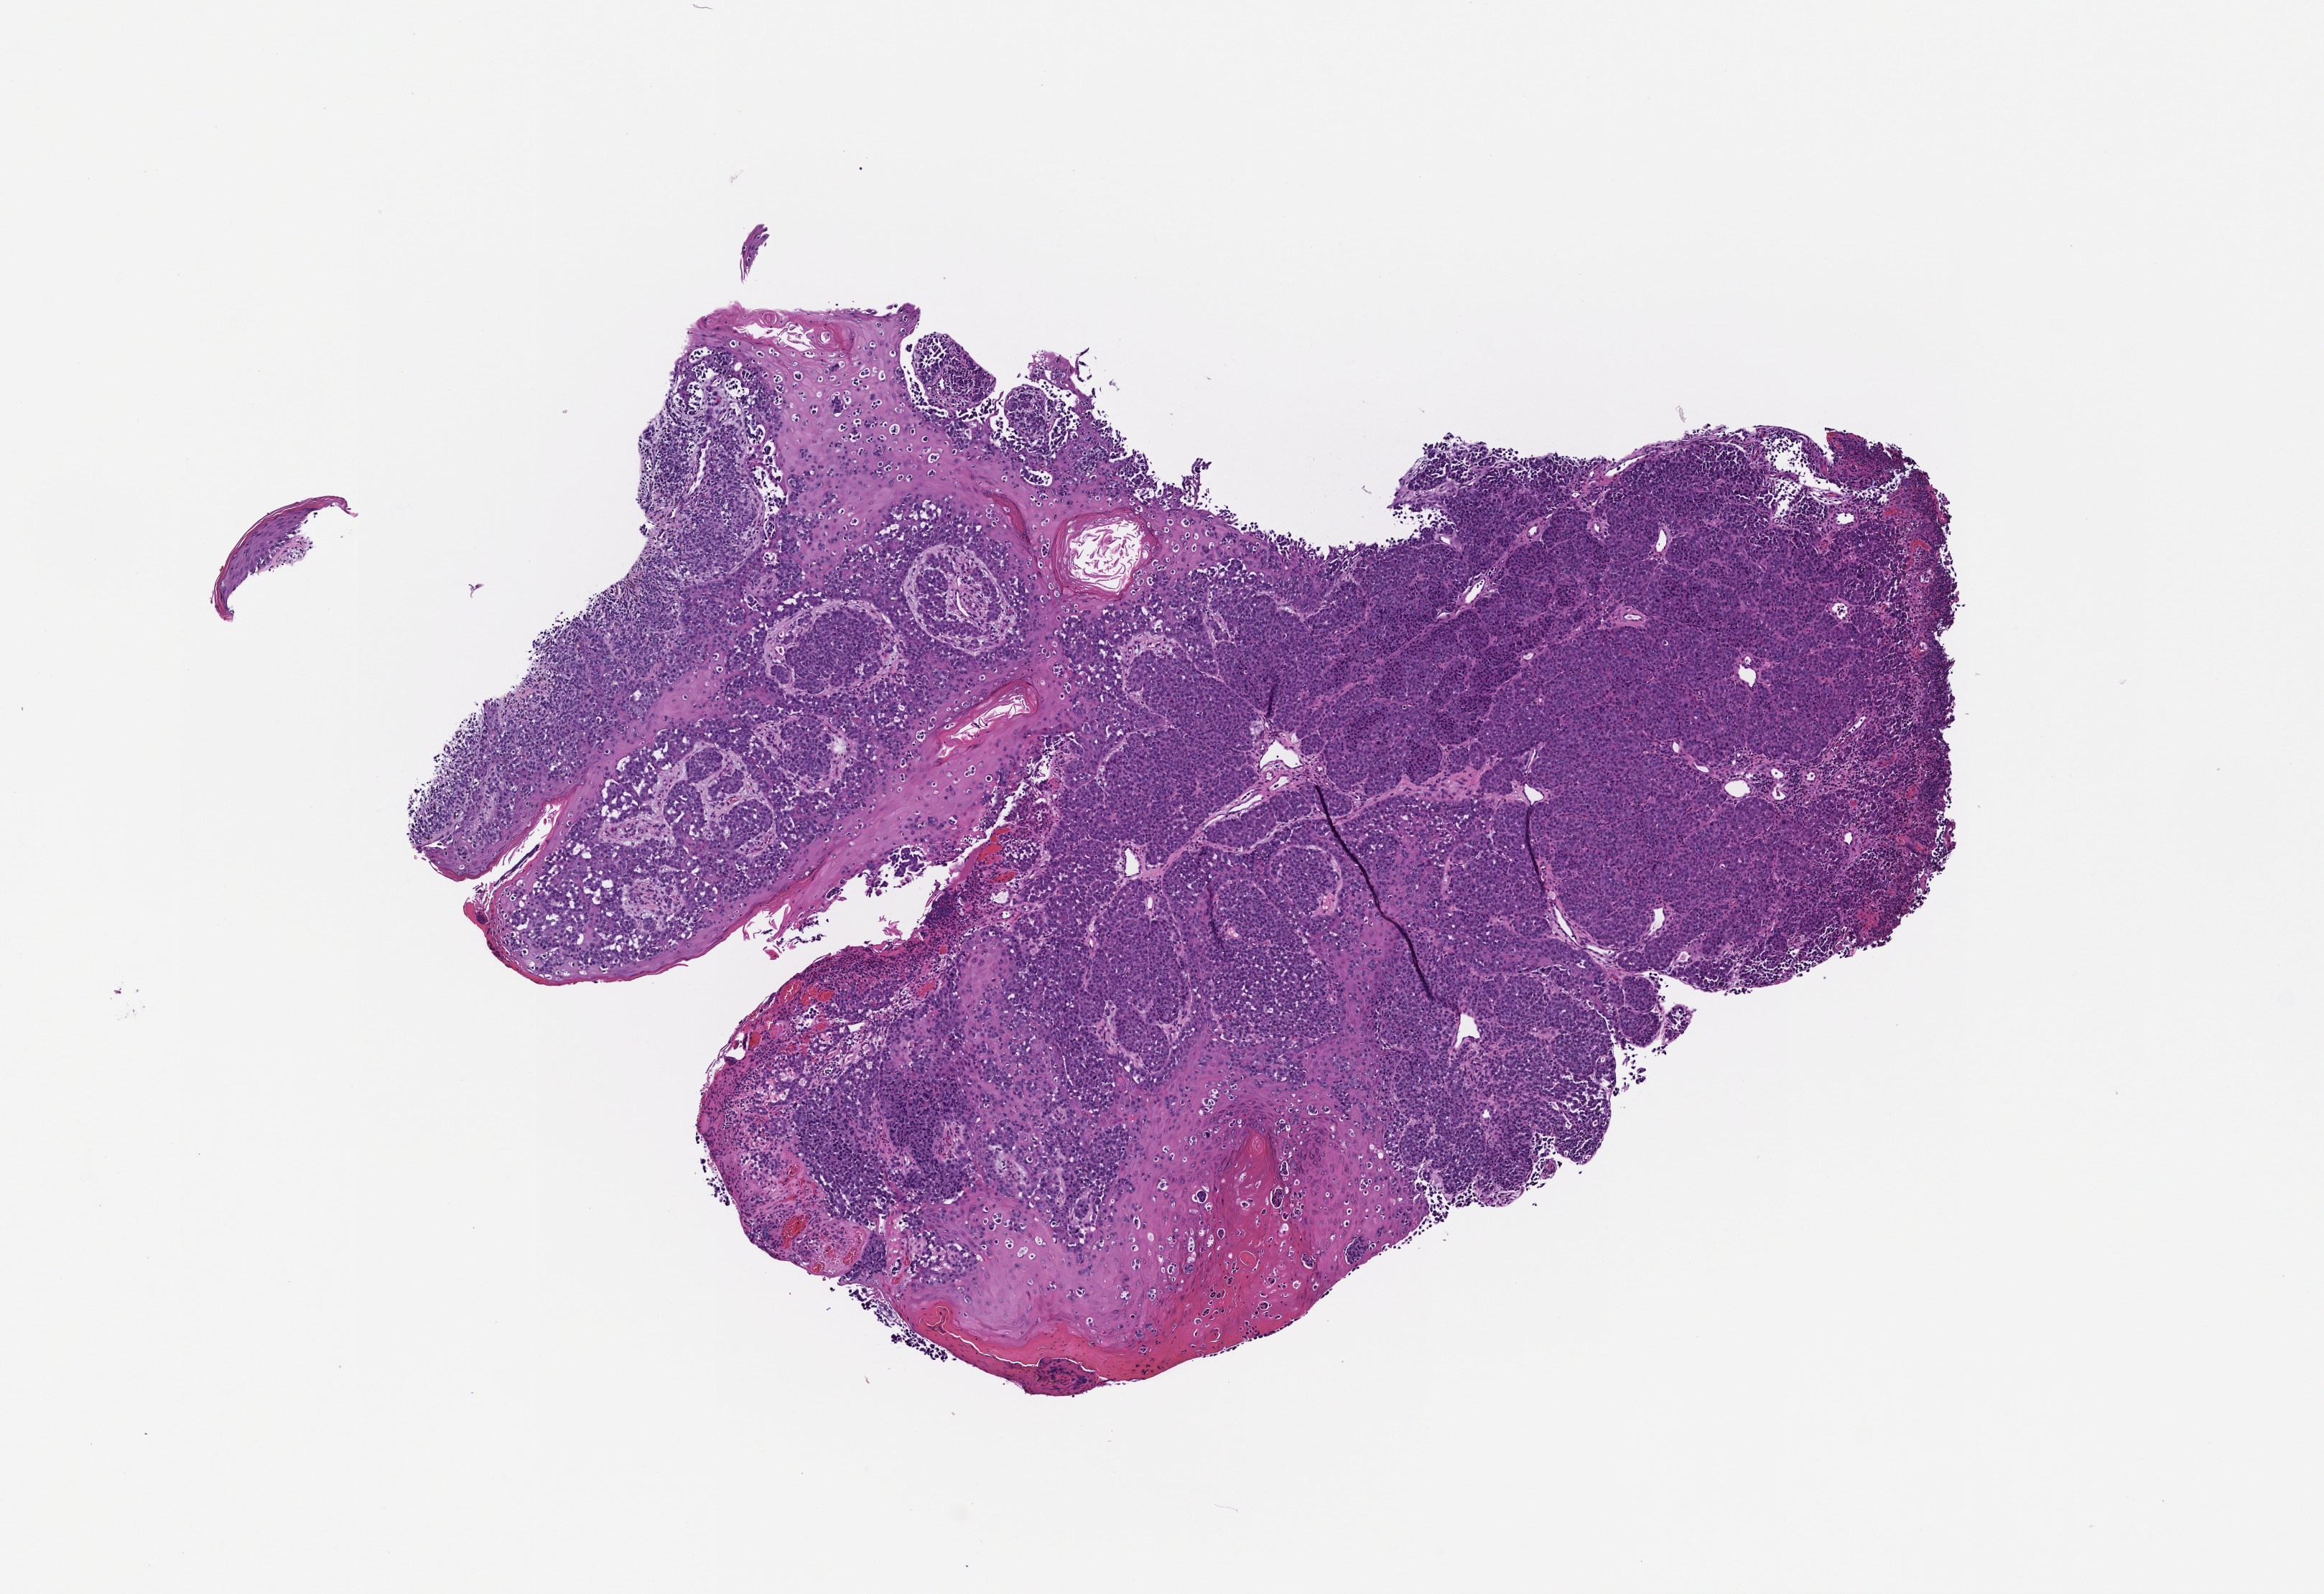
Digitized haematoxylin and eosin-stained section — shown as a low-resolution overview of the whole scanned area (about 6.5 x 4.5 mm). Formalin-fixed, paraffin-embedded (FFPE) tissue. Site: skin. Patient sex: male.
* this section: primary tumour tissue
* diagnosis: Melanoma